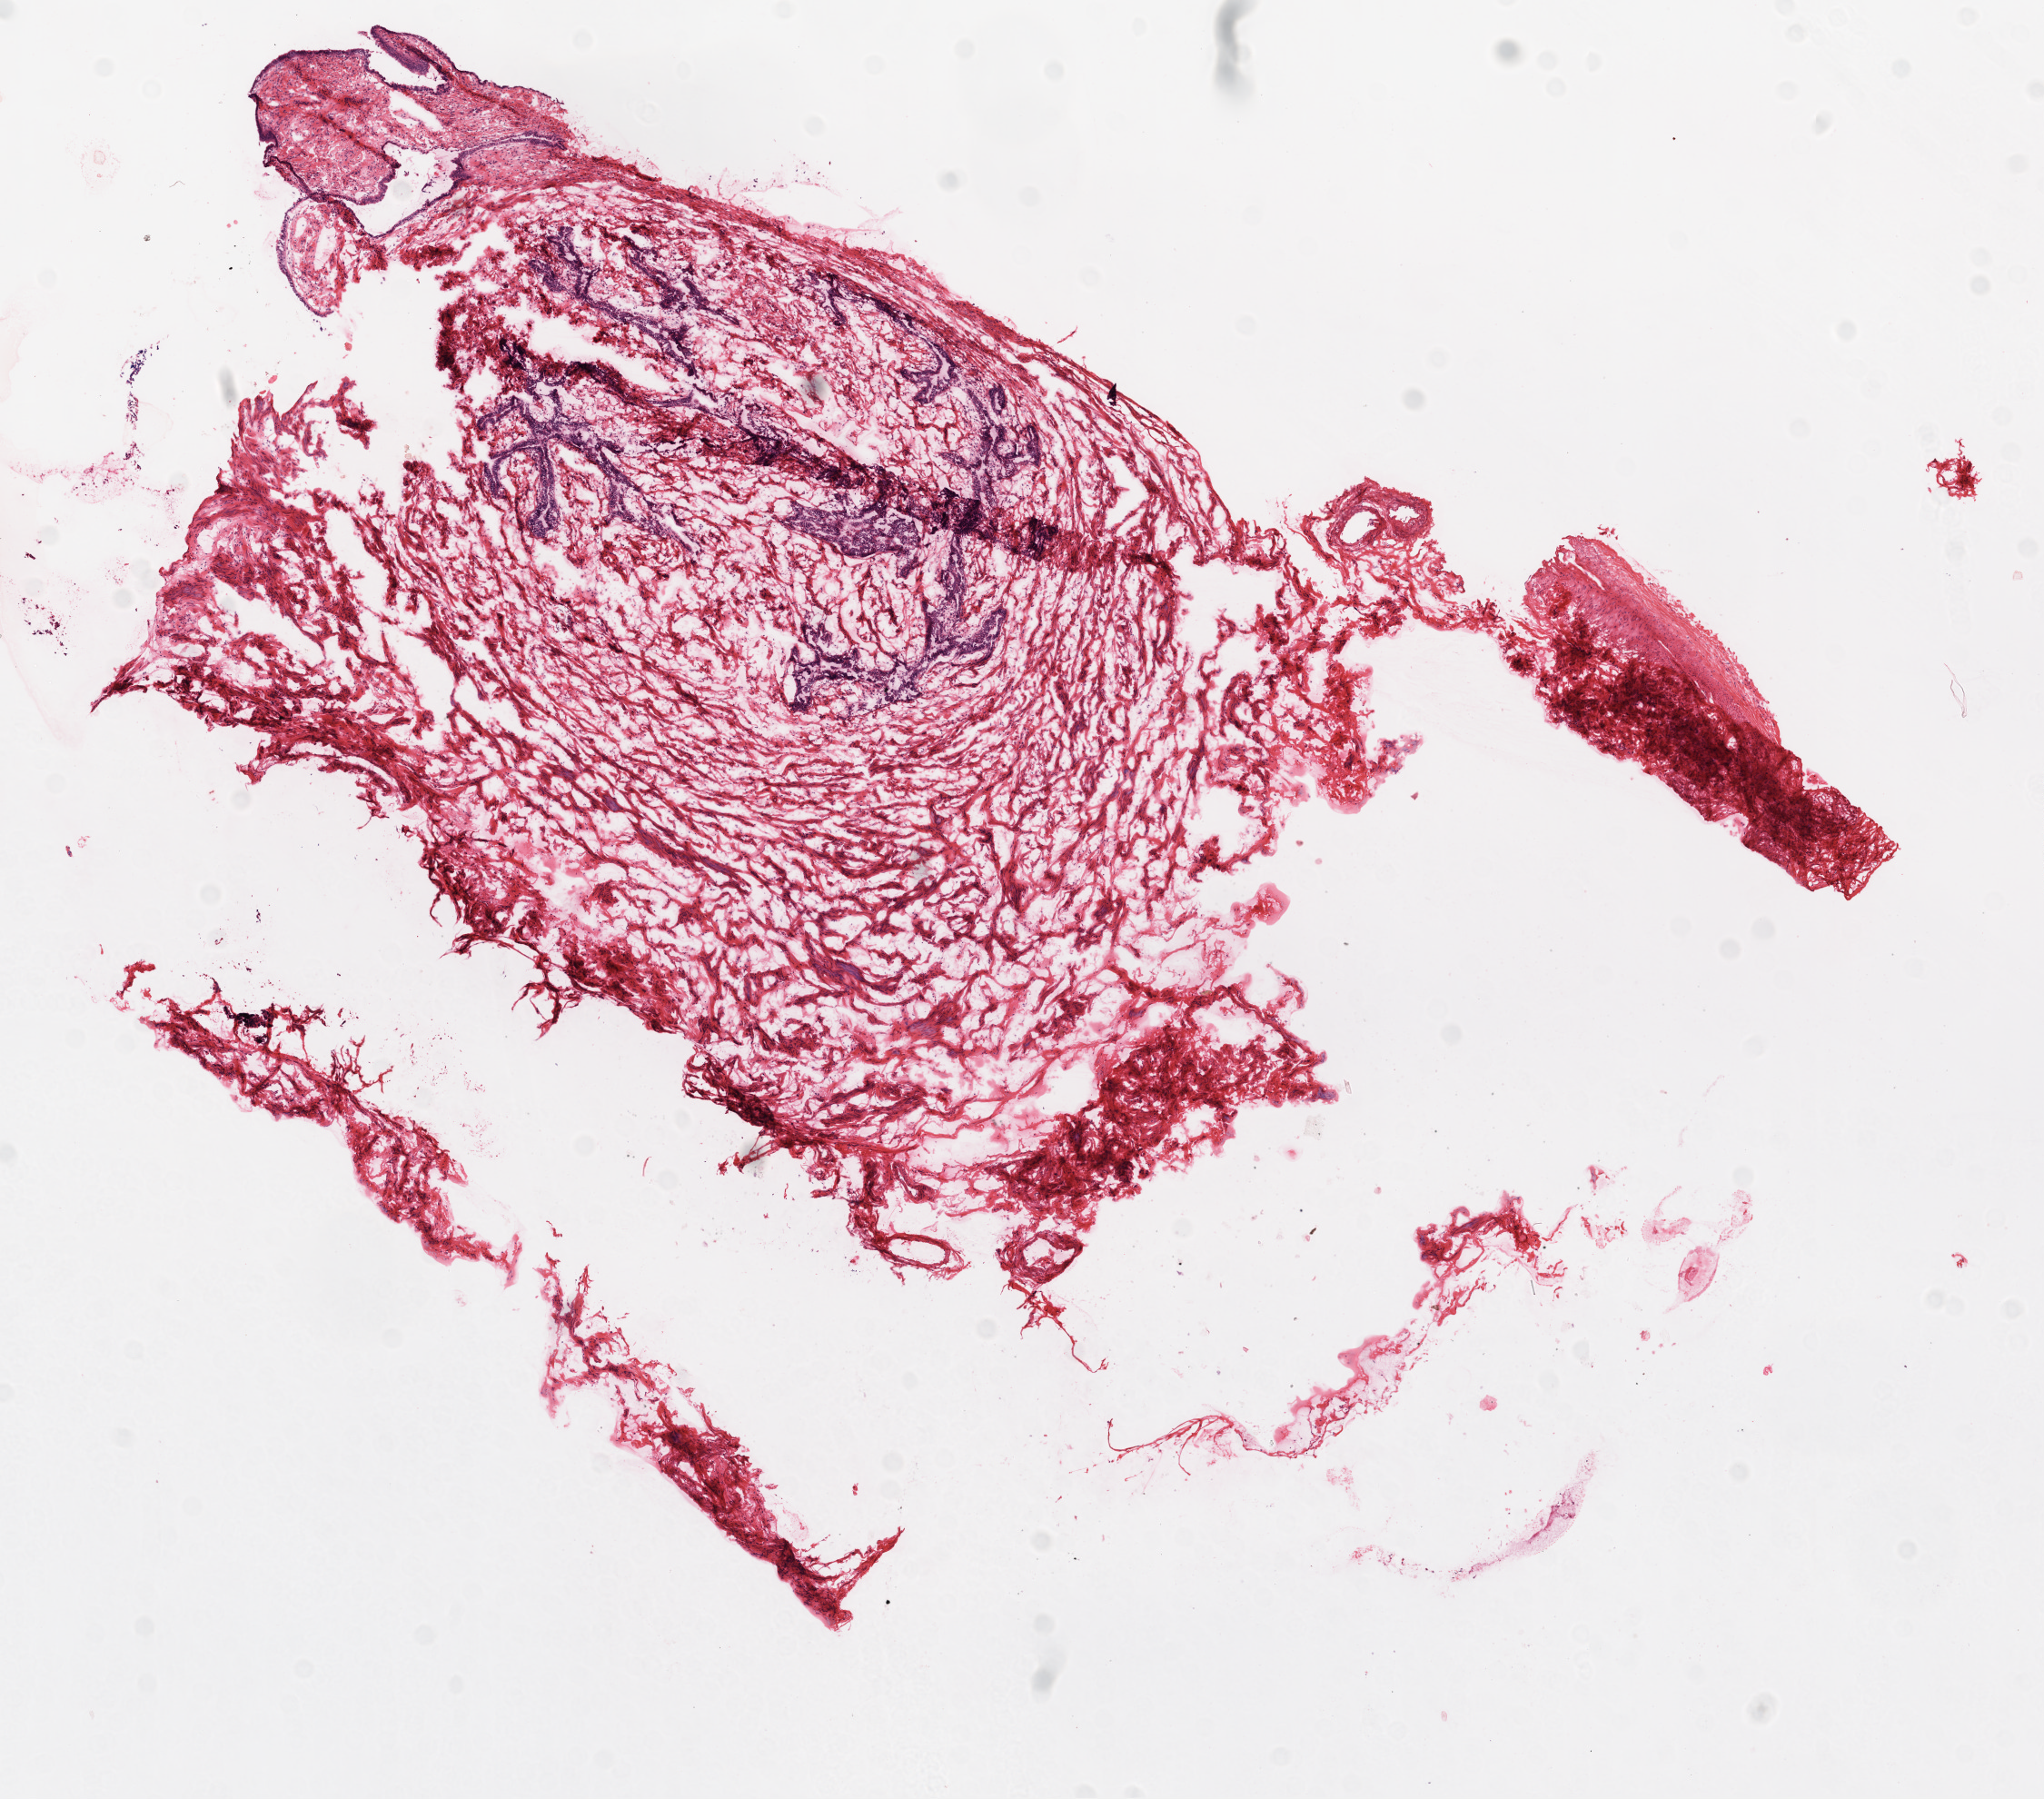
H&E whole-slide image — shown as a low-resolution overview of the whole scanned area (about 9.0 x 7.9 mm), frozen section from the top of the tissue portion, solid tissue normal (non-tumour tissue) sample from the ovary. Patient: female, age at initial diagnosis 61 years.
- this section: solid tissue normal sample (biorepository sample class)
- patient diagnosis: Serous cystadenocarcinoma, NOS